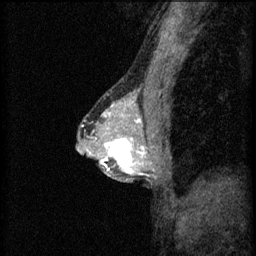
Breast MRI (dynamic contrast-enhanced), one sagittal slice. Position 36 of 60 along the scan axis. 3 images stored at this slice position (order not interpretable as contrast timing). 1.5 T. TE 4.2 ms, TR 8.2 ms. 256 × 256 image matrix, field of view 180 × 180 mm. Patient: female, 44 years.
Annotated regions visible in this slice (semi-automatically segmented with operator editing):
- analysis volume of interest (the breast-tissue region the enhancement analysis was run in; not a lesion): box from (x=102, y=132) to (x=151, y=181) px
- tumour enhancement mask (voxels above the 70 % enhancement threshold inside the analysis volume of interest): (x=102, y=138)–(x=151, y=177)